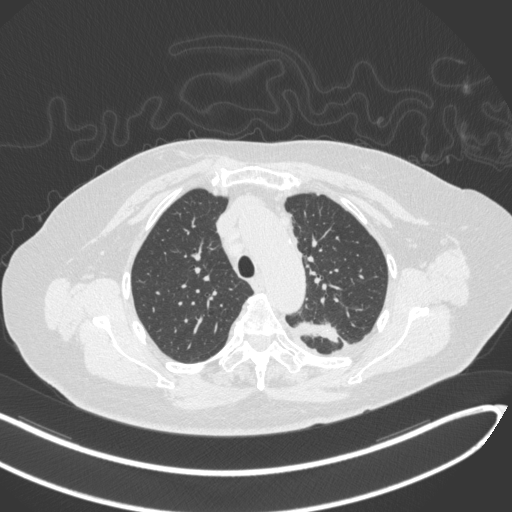
Chest CT, one axial slice; slice 237 of 270 in the series (ordered by position); reconstruction kernel B31f; lung window (W 1500 / L -600 HU); 1 mm slice thickness; 512 × 512 image matrix, field of view 400 × 400 mm. Female patient, age 76 years. From the clinical record (not read from this slice): clinical TNM (as recorded): T1c N0 M0.
Outlined on this slice (bounding box drawn by a radiologist):
- lung tumour (recorded histology: adenocarcinoma): bounding box [x1, y1, x2, y2] px = [289, 314, 340, 346]